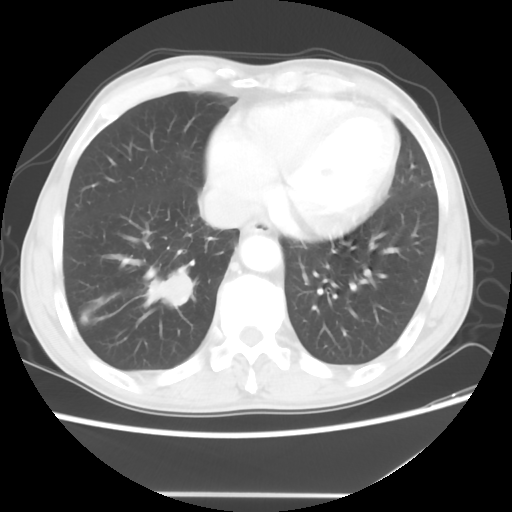
Chest CT, one axial slice. Position 14 of 56 along the scan axis. Lung window (W 1500 / L -600 HU). 5 mm slice thickness. 512 × 512 image matrix, field of view 344 × 344 mm. Patient: male, 65 years. From the clinical record (not read from this slice): clinical TNM (as recorded): T1c N3 M0.
Annotated regions visible in this slice (rectangle marked by the reading radiologist):
- lung tumour (recorded histology: small cell carcinoma): box from (x=136, y=262) to (x=201, y=309) px